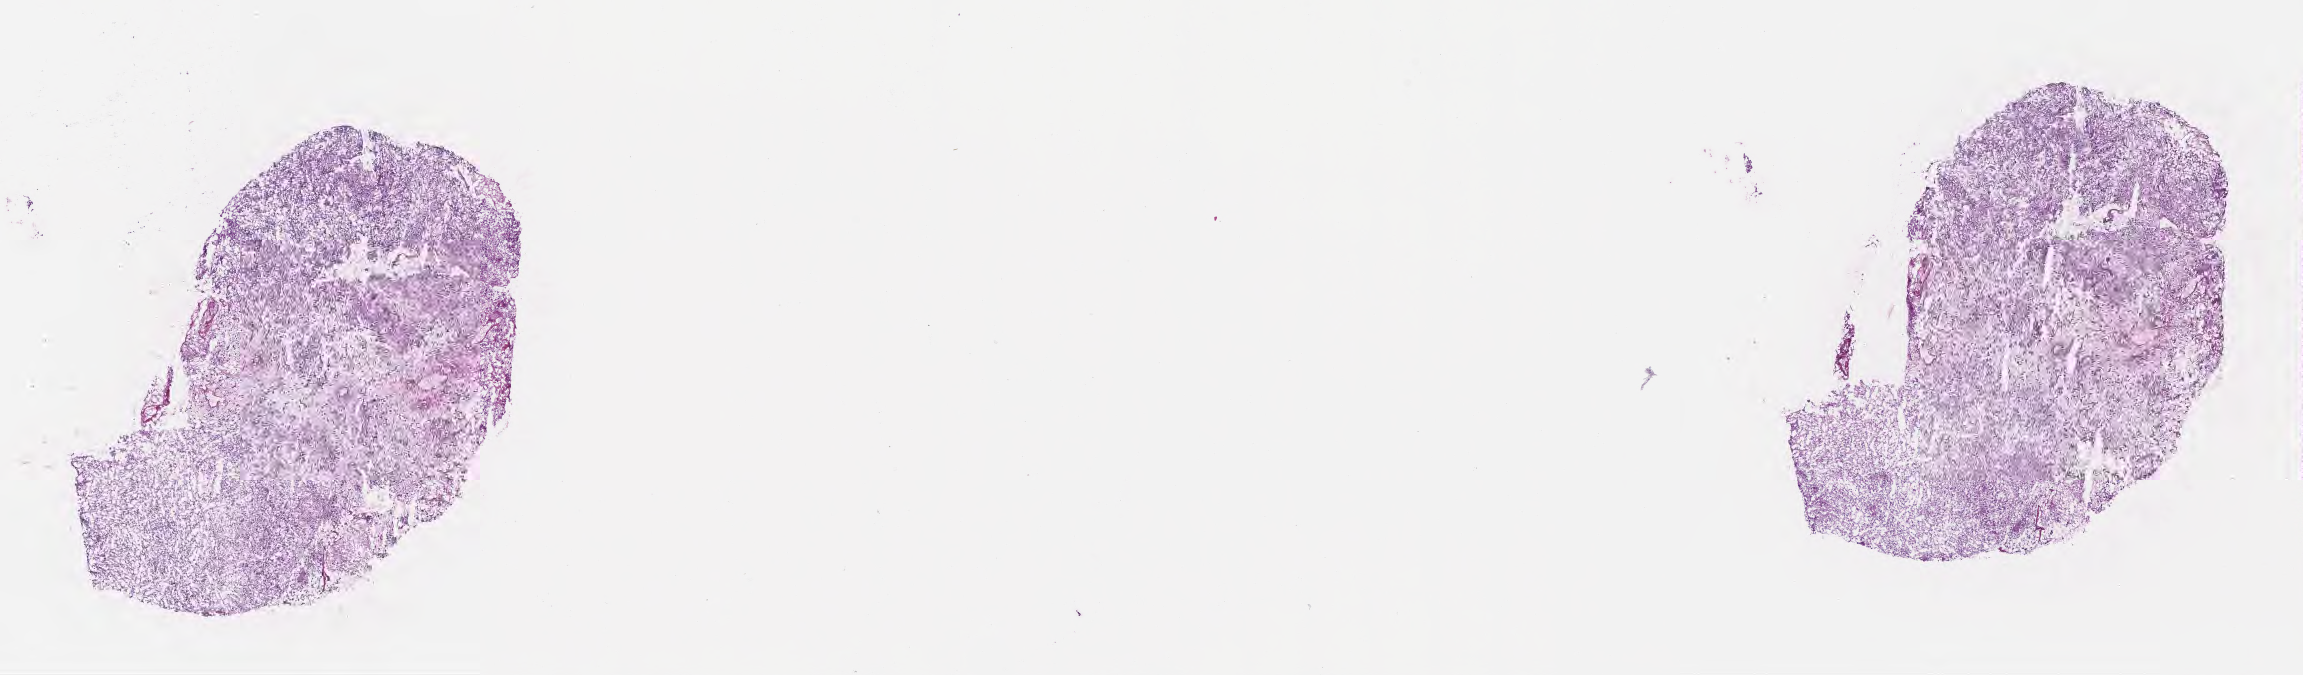
Haematoxylin and eosin whole-slide image, low-resolution overview of the scanned area, about 18.6 x 5.5 mm; frozen section (tissue freezing medium); primary tumor; anatomic site: brain. Patient: female, age at initial diagnosis 56 years. Slide review estimates, as recorded: tumor cells 77%, tumor nuclei 94%, stromal cells 3%, necrosis 15%, normal cells 5%. Inflammatory infiltration, as recorded: lymphocyte infiltration 0%, monocyte infiltration 0%, neutrophil infiltration 0%.
Diagnosis: Glioblastoma, NOS. Section: top of the tissue portion.